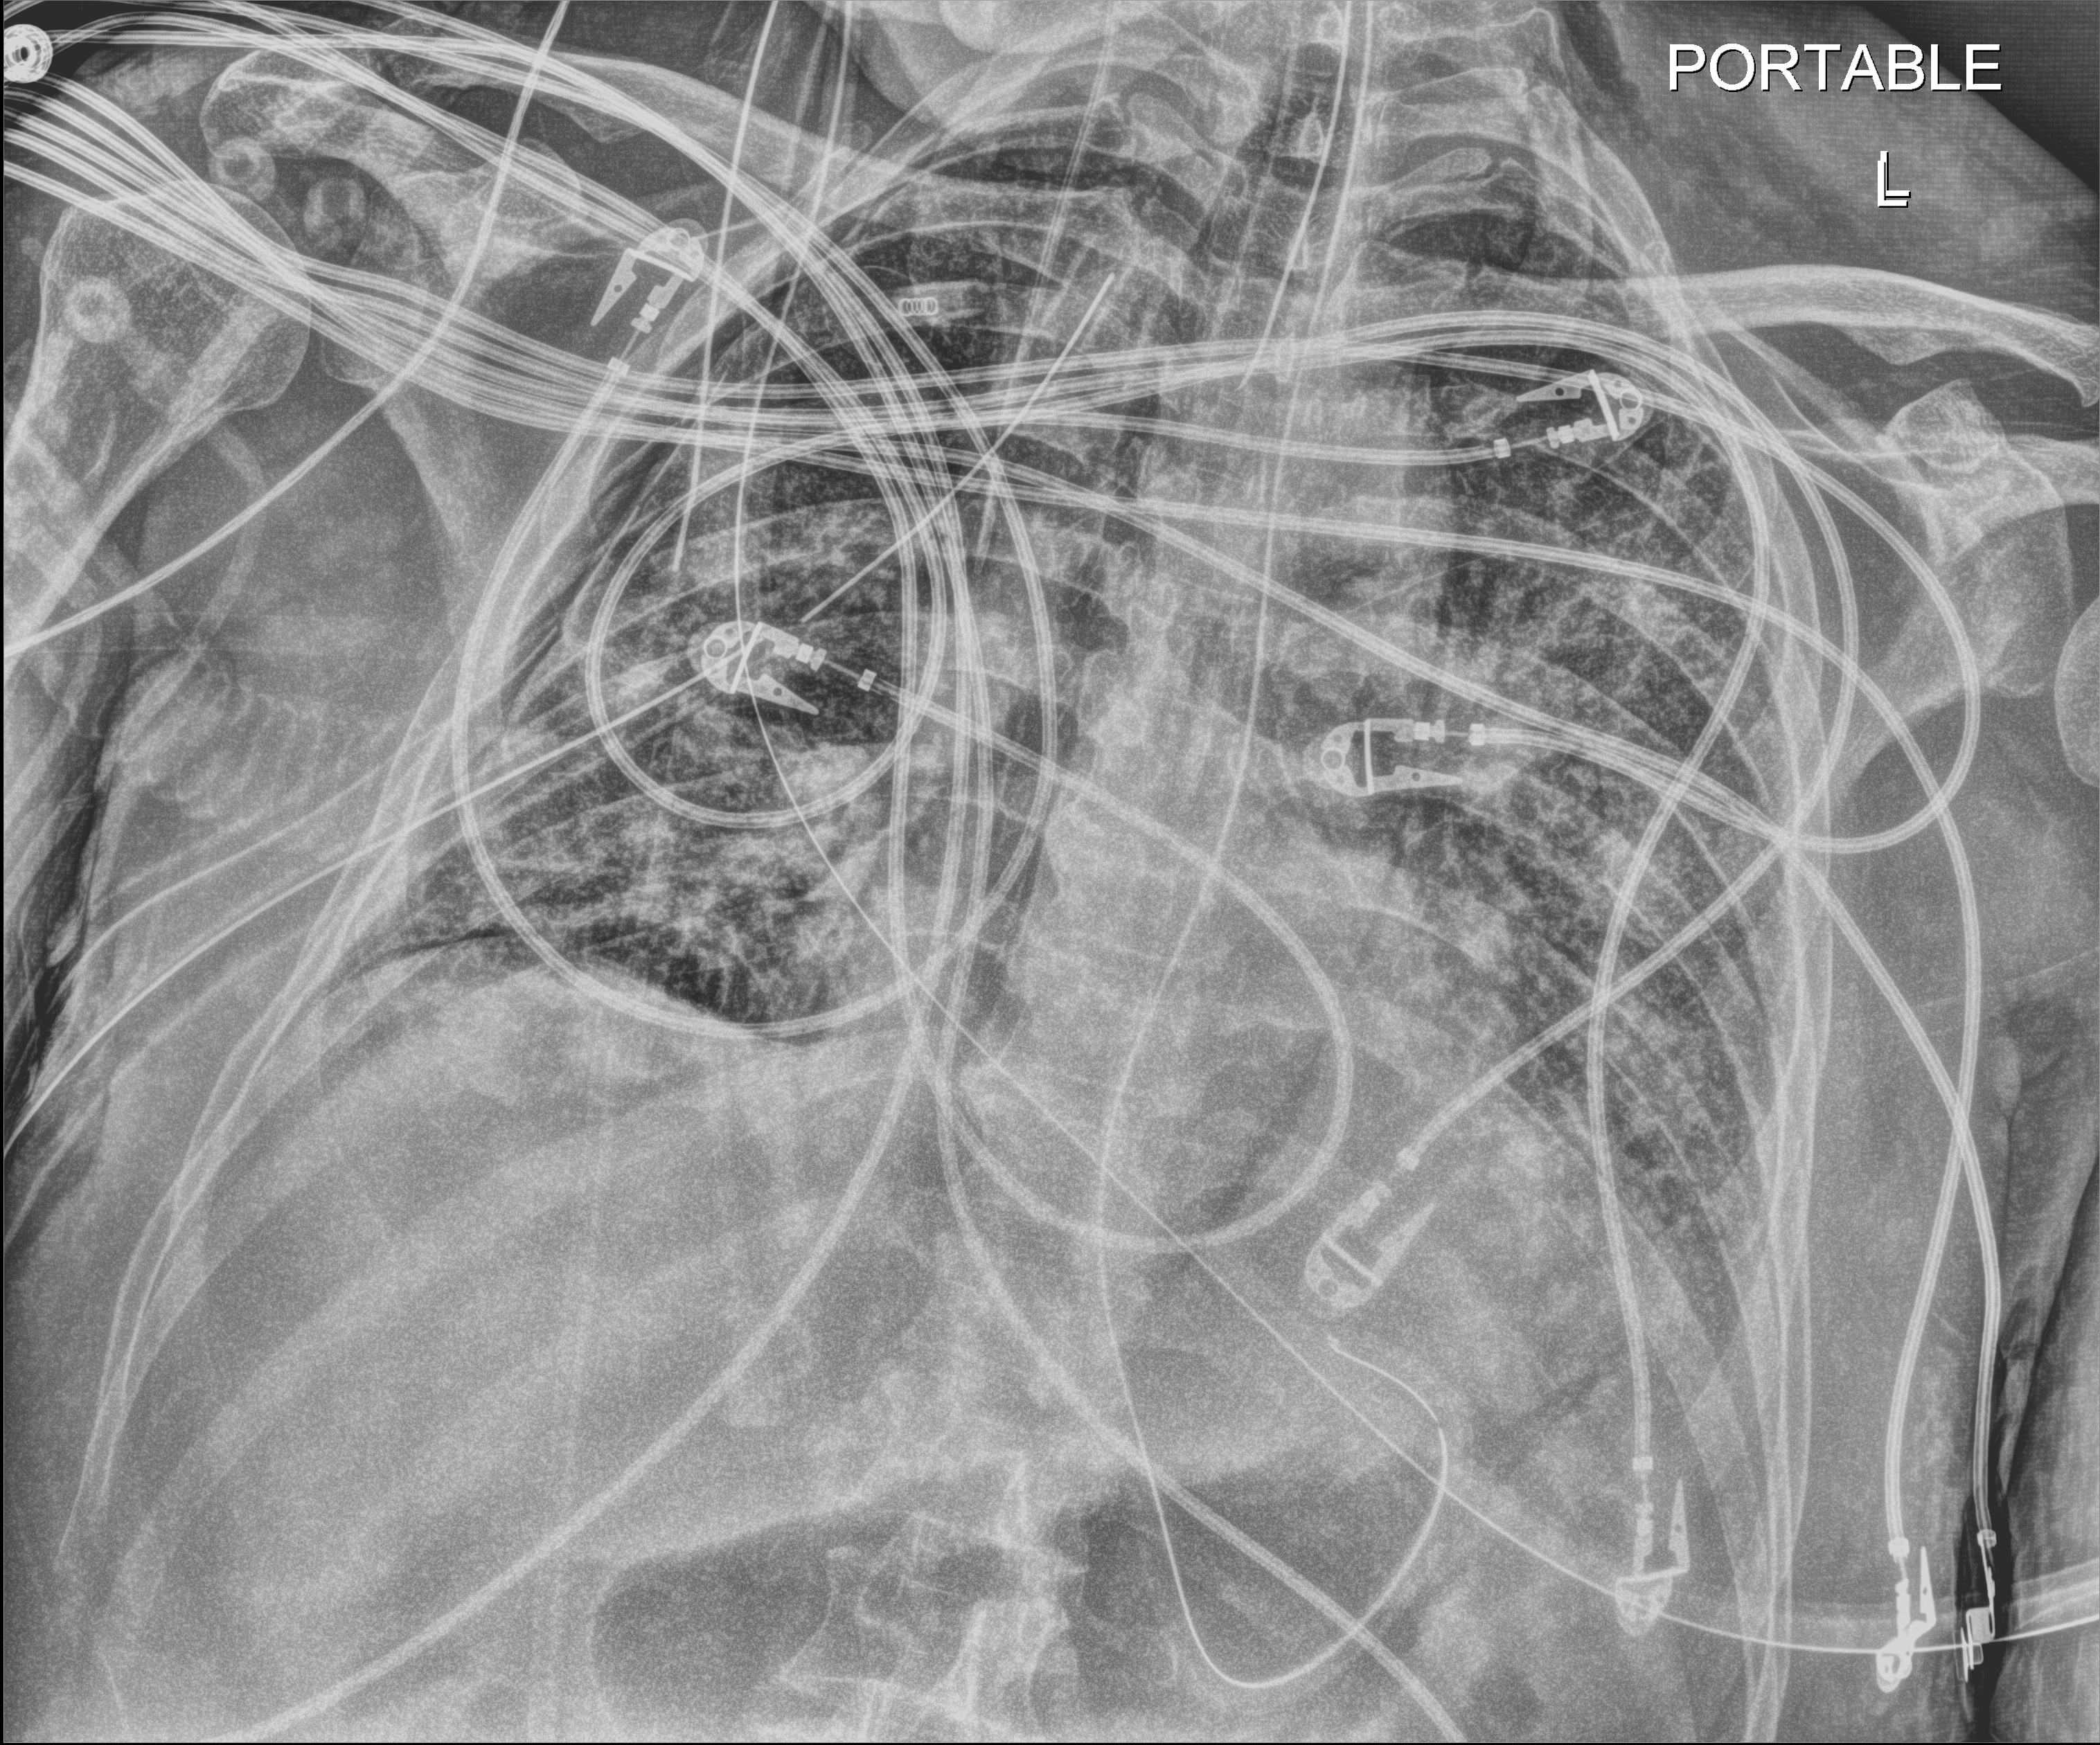
Chest X-ray (portable); anteroposterior (AP) projection. Male patient hospitalised with COVID-19, age 60–74 years.
Admission-level facts for this patient (not findings on this image; timing relative to this image not recorded):
- admitted to intensive care during this hospital stay: yes